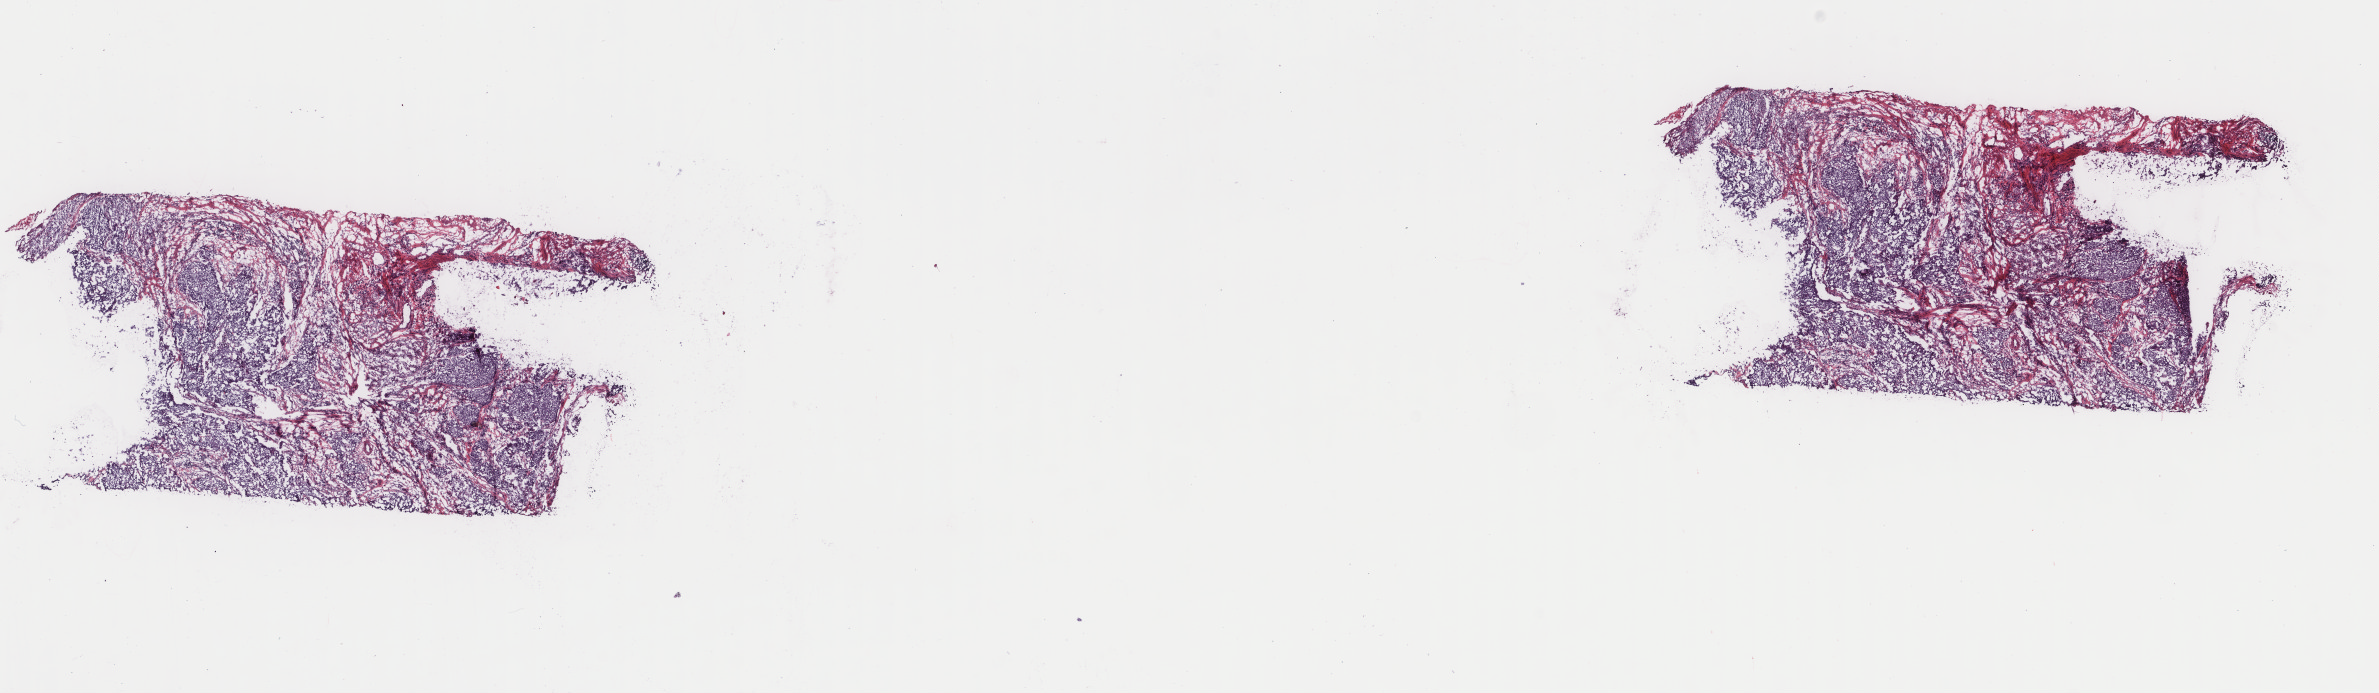
H&E-stained whole-slide image — shown as a low-resolution overview of the whole scanned area (about 18.9 x 5.5 mm), frozen section, sample: primary tumour, cervix. Female patient; age at initial diagnosis 52 years. Histologic grade: G1 (well differentiated). Slide review estimates, as recorded: tumour cells 100%, tumour nuclei 80%, normal cells 0%, stromal cells 0%, necrosis 0%. Infiltration values recorded for this section: lymphocyte infiltration 2%, monocyte infiltration 0%, neutrophil infiltration 0%.
FIGO stage: IA. Diagnosis: Squamous cell carcinoma, keratinizing, NOS (cervix uteri).